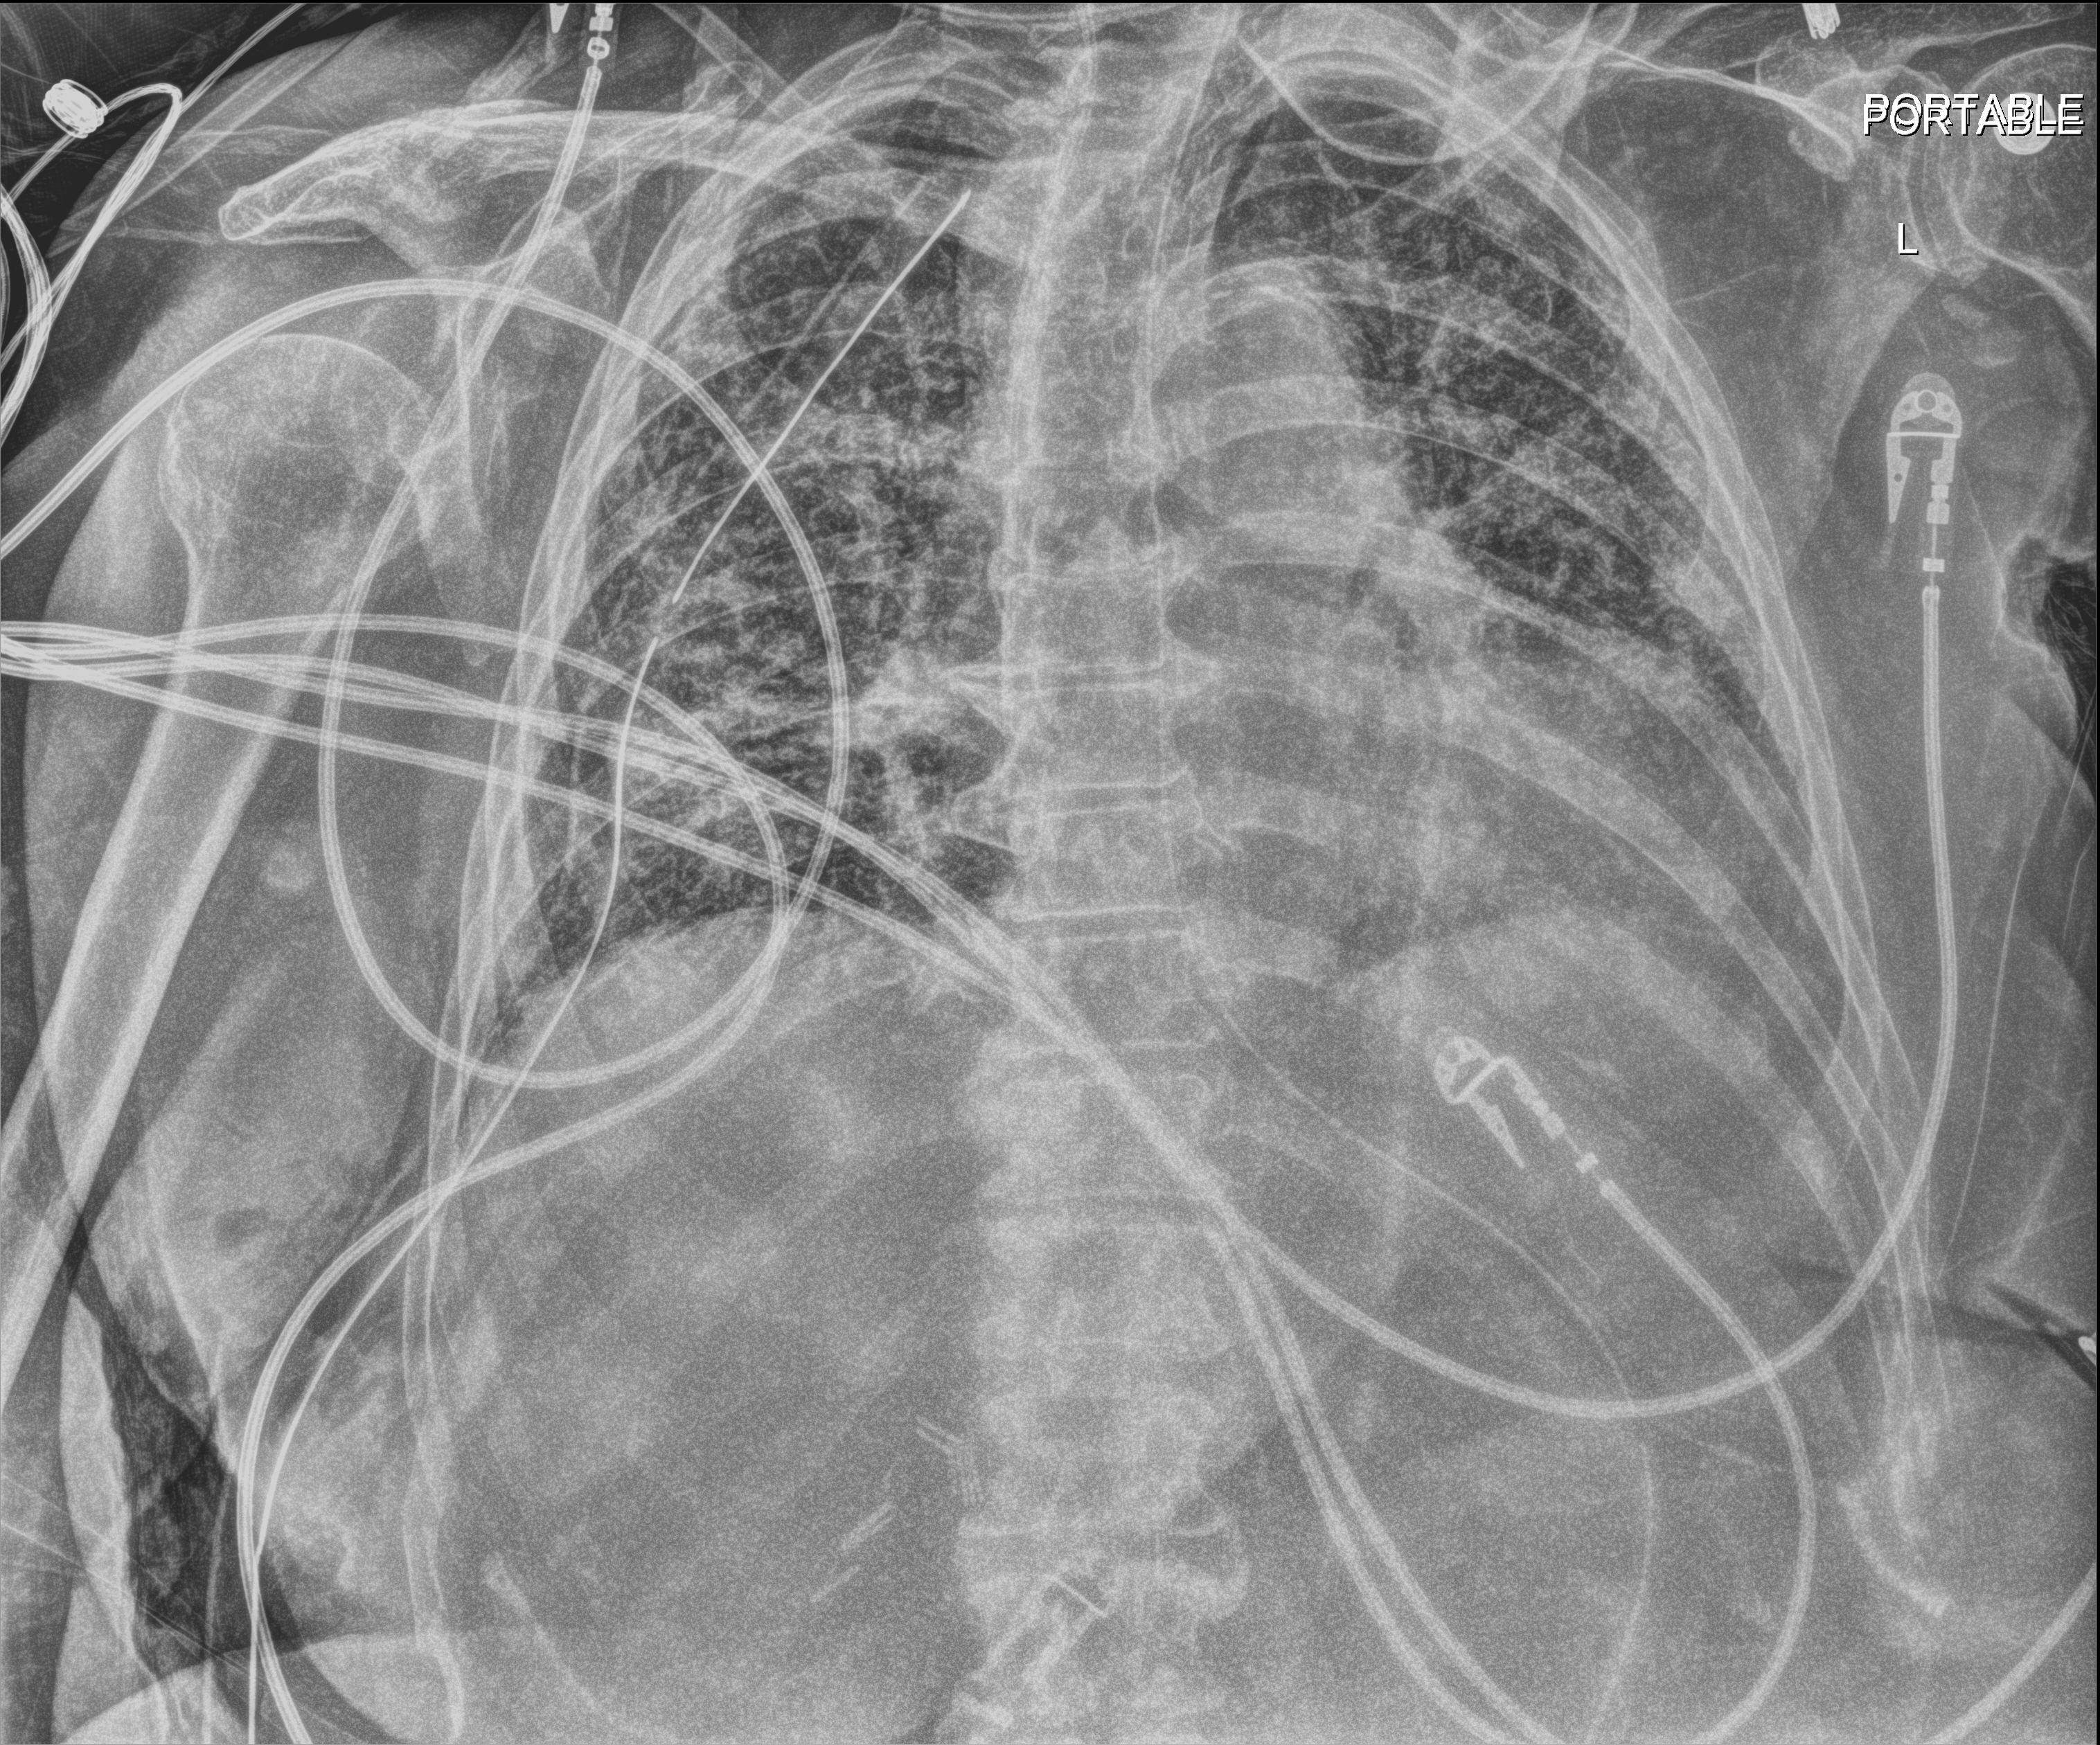
Portable chest radiograph. Patient hospitalised with COVID-19; female, aged 75–90 years.
Admission-level facts for this patient (not findings on this image; timing relative to this image not recorded):
- mechanically ventilated during this hospital stay: yes
- admitted to intensive care during this hospital stay: no